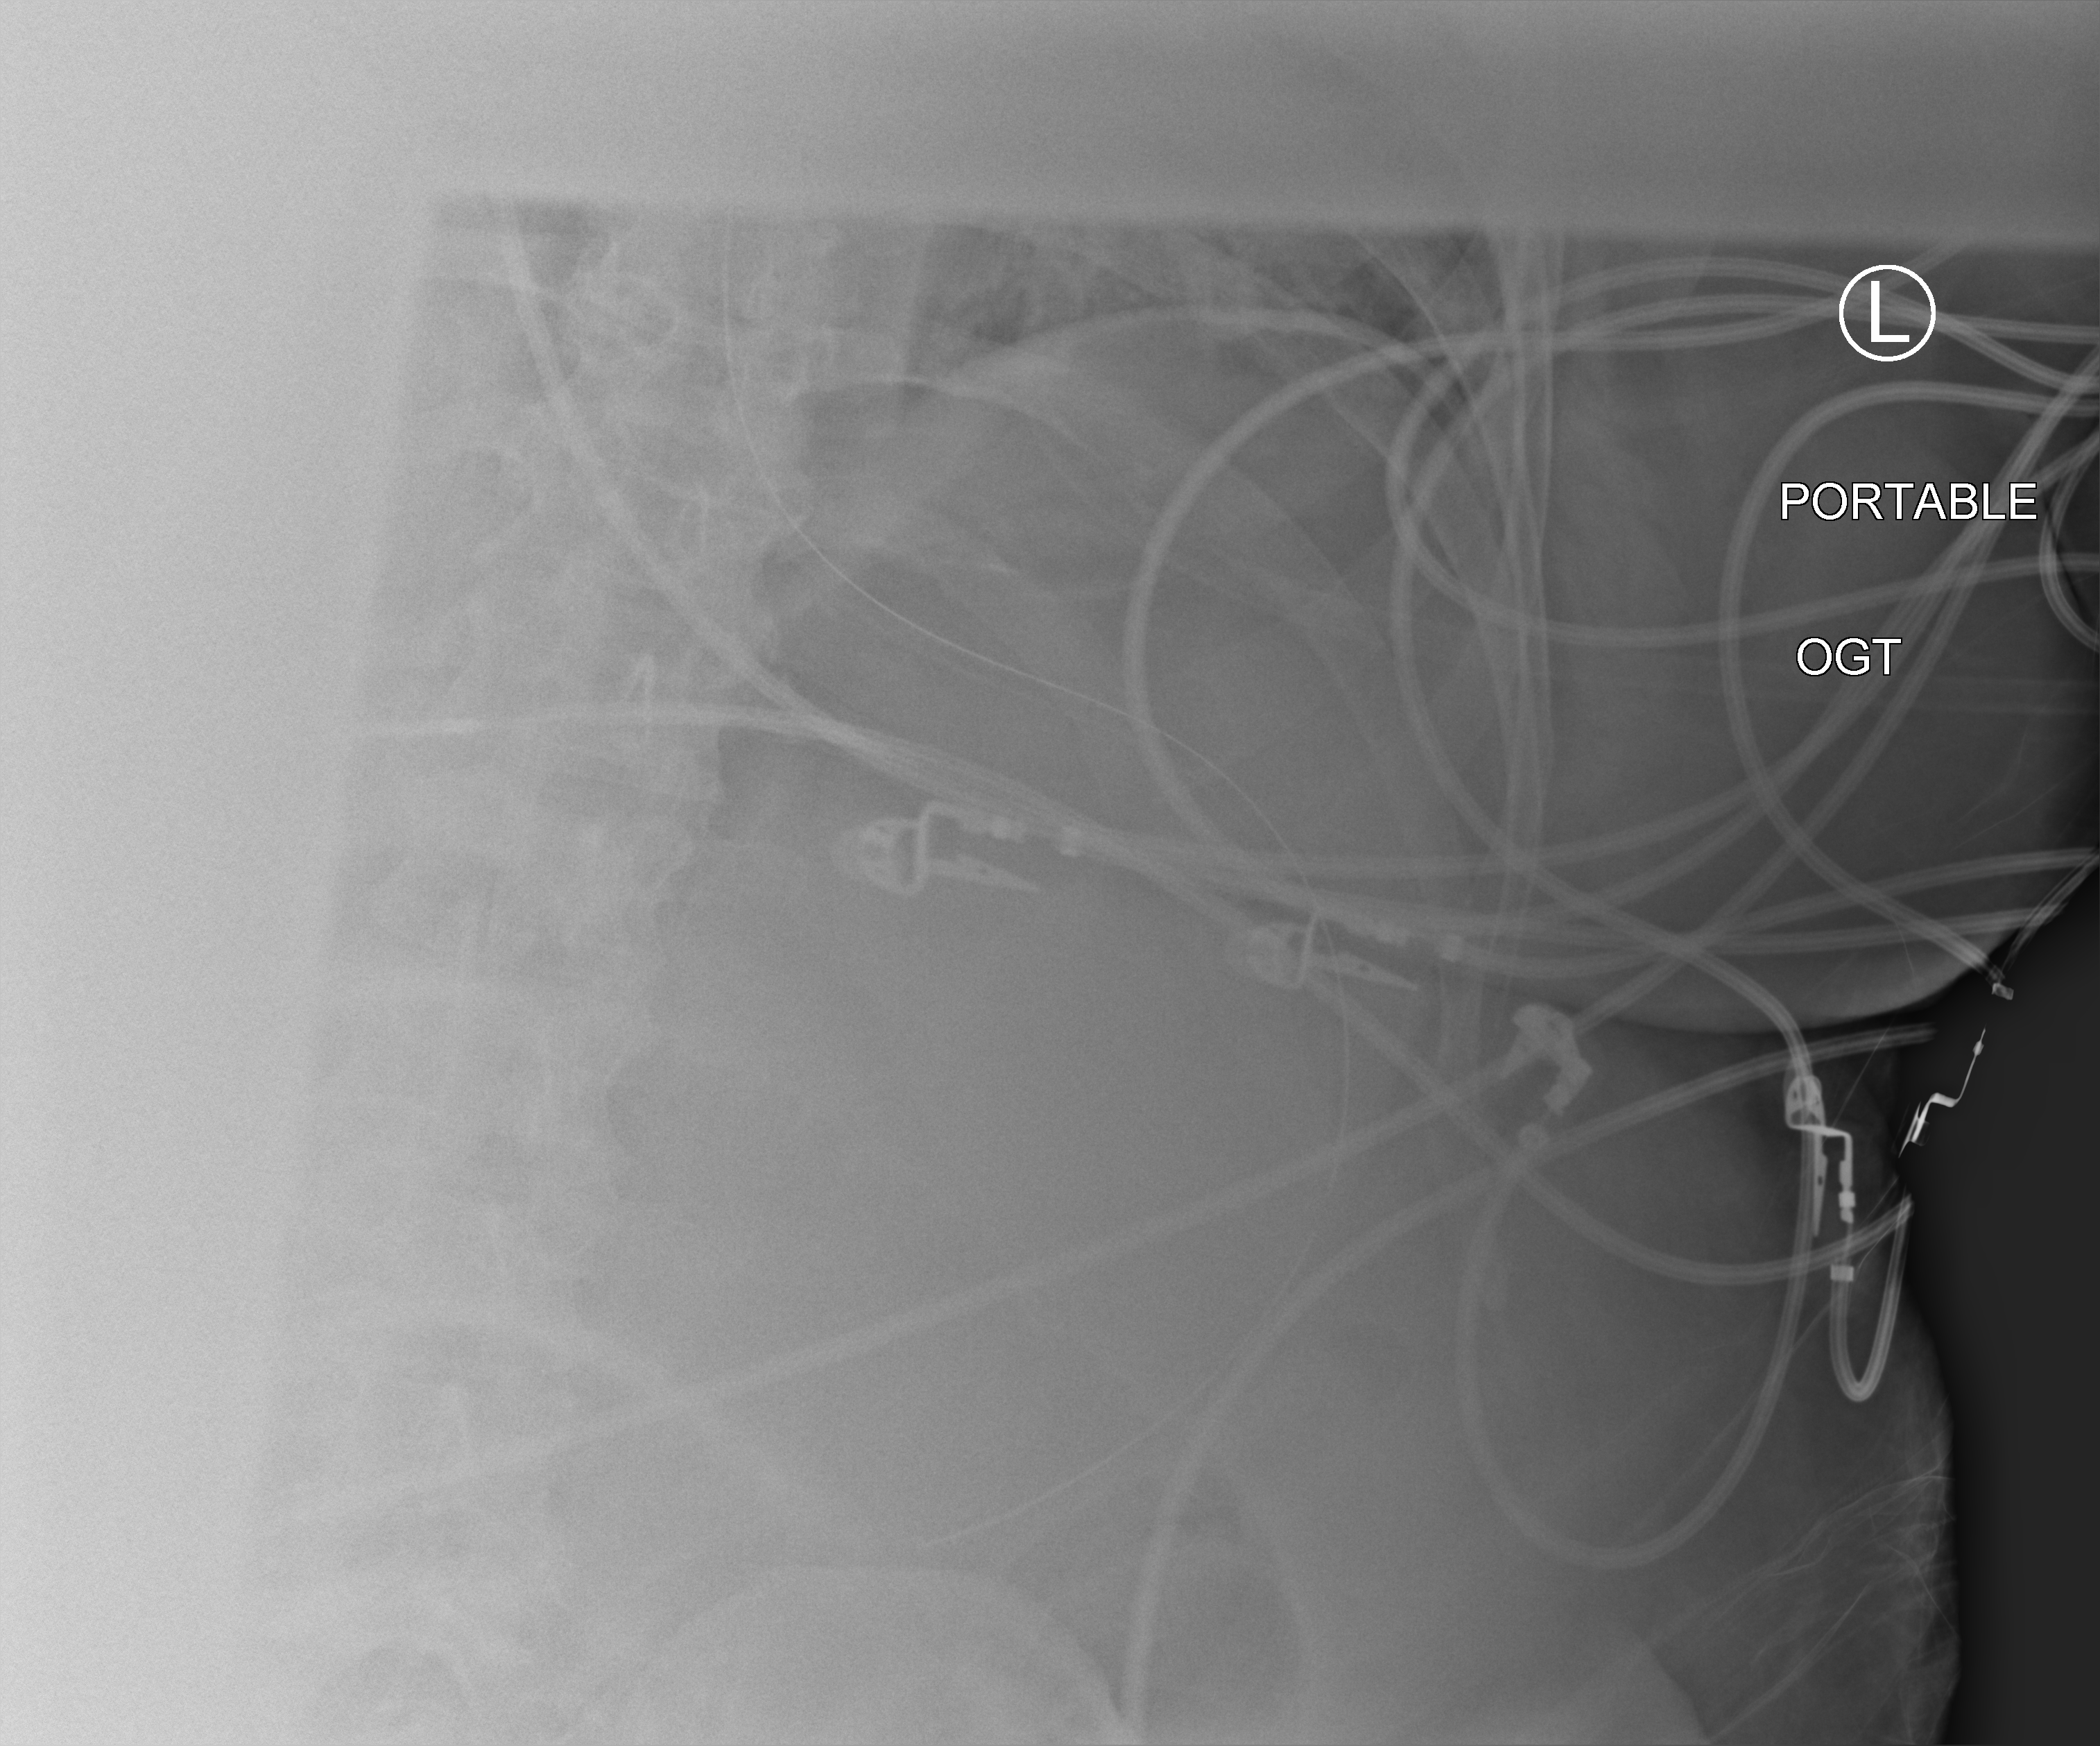
Portable chest radiograph. Patient hospitalised with COVID-19; male, aged 18–59 years.
Hospital-stay facts (about this admission, not read from this image; timing relative to this image not recorded):
- admitted to intensive care during this hospital stay: yes
- length of hospital stay: 28 days